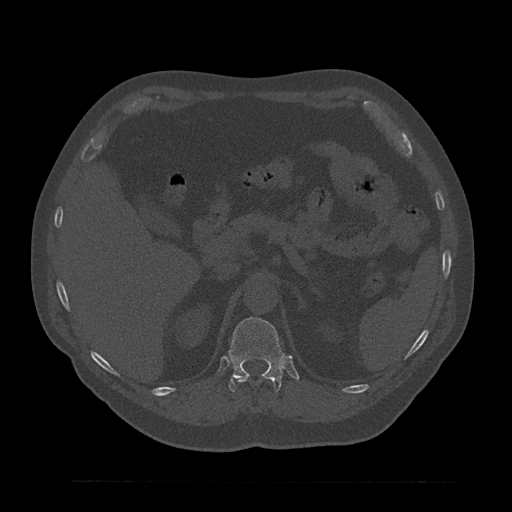
CT including the spine, one axial slice. Position 248 of 797 along the scan axis. Reconstruction kernel Br40s/3. 120 kVp. Bone window (W 1800 / L 400 HU). 0.5 mm slice thickness. 512 × 512 image matrix, field of view 430 × 430 mm. Patient: male, 61 years. From the clinical record (not read from this slice): primary cancer: prostate.
Structures marked on this image (semi-automatically segmented with operator editing):
- T11 vertebra: bounding box [x1, y1, x2, y2] px = [237, 378, 271, 383]
- T12 vertebra: [228, 317, 285, 392]